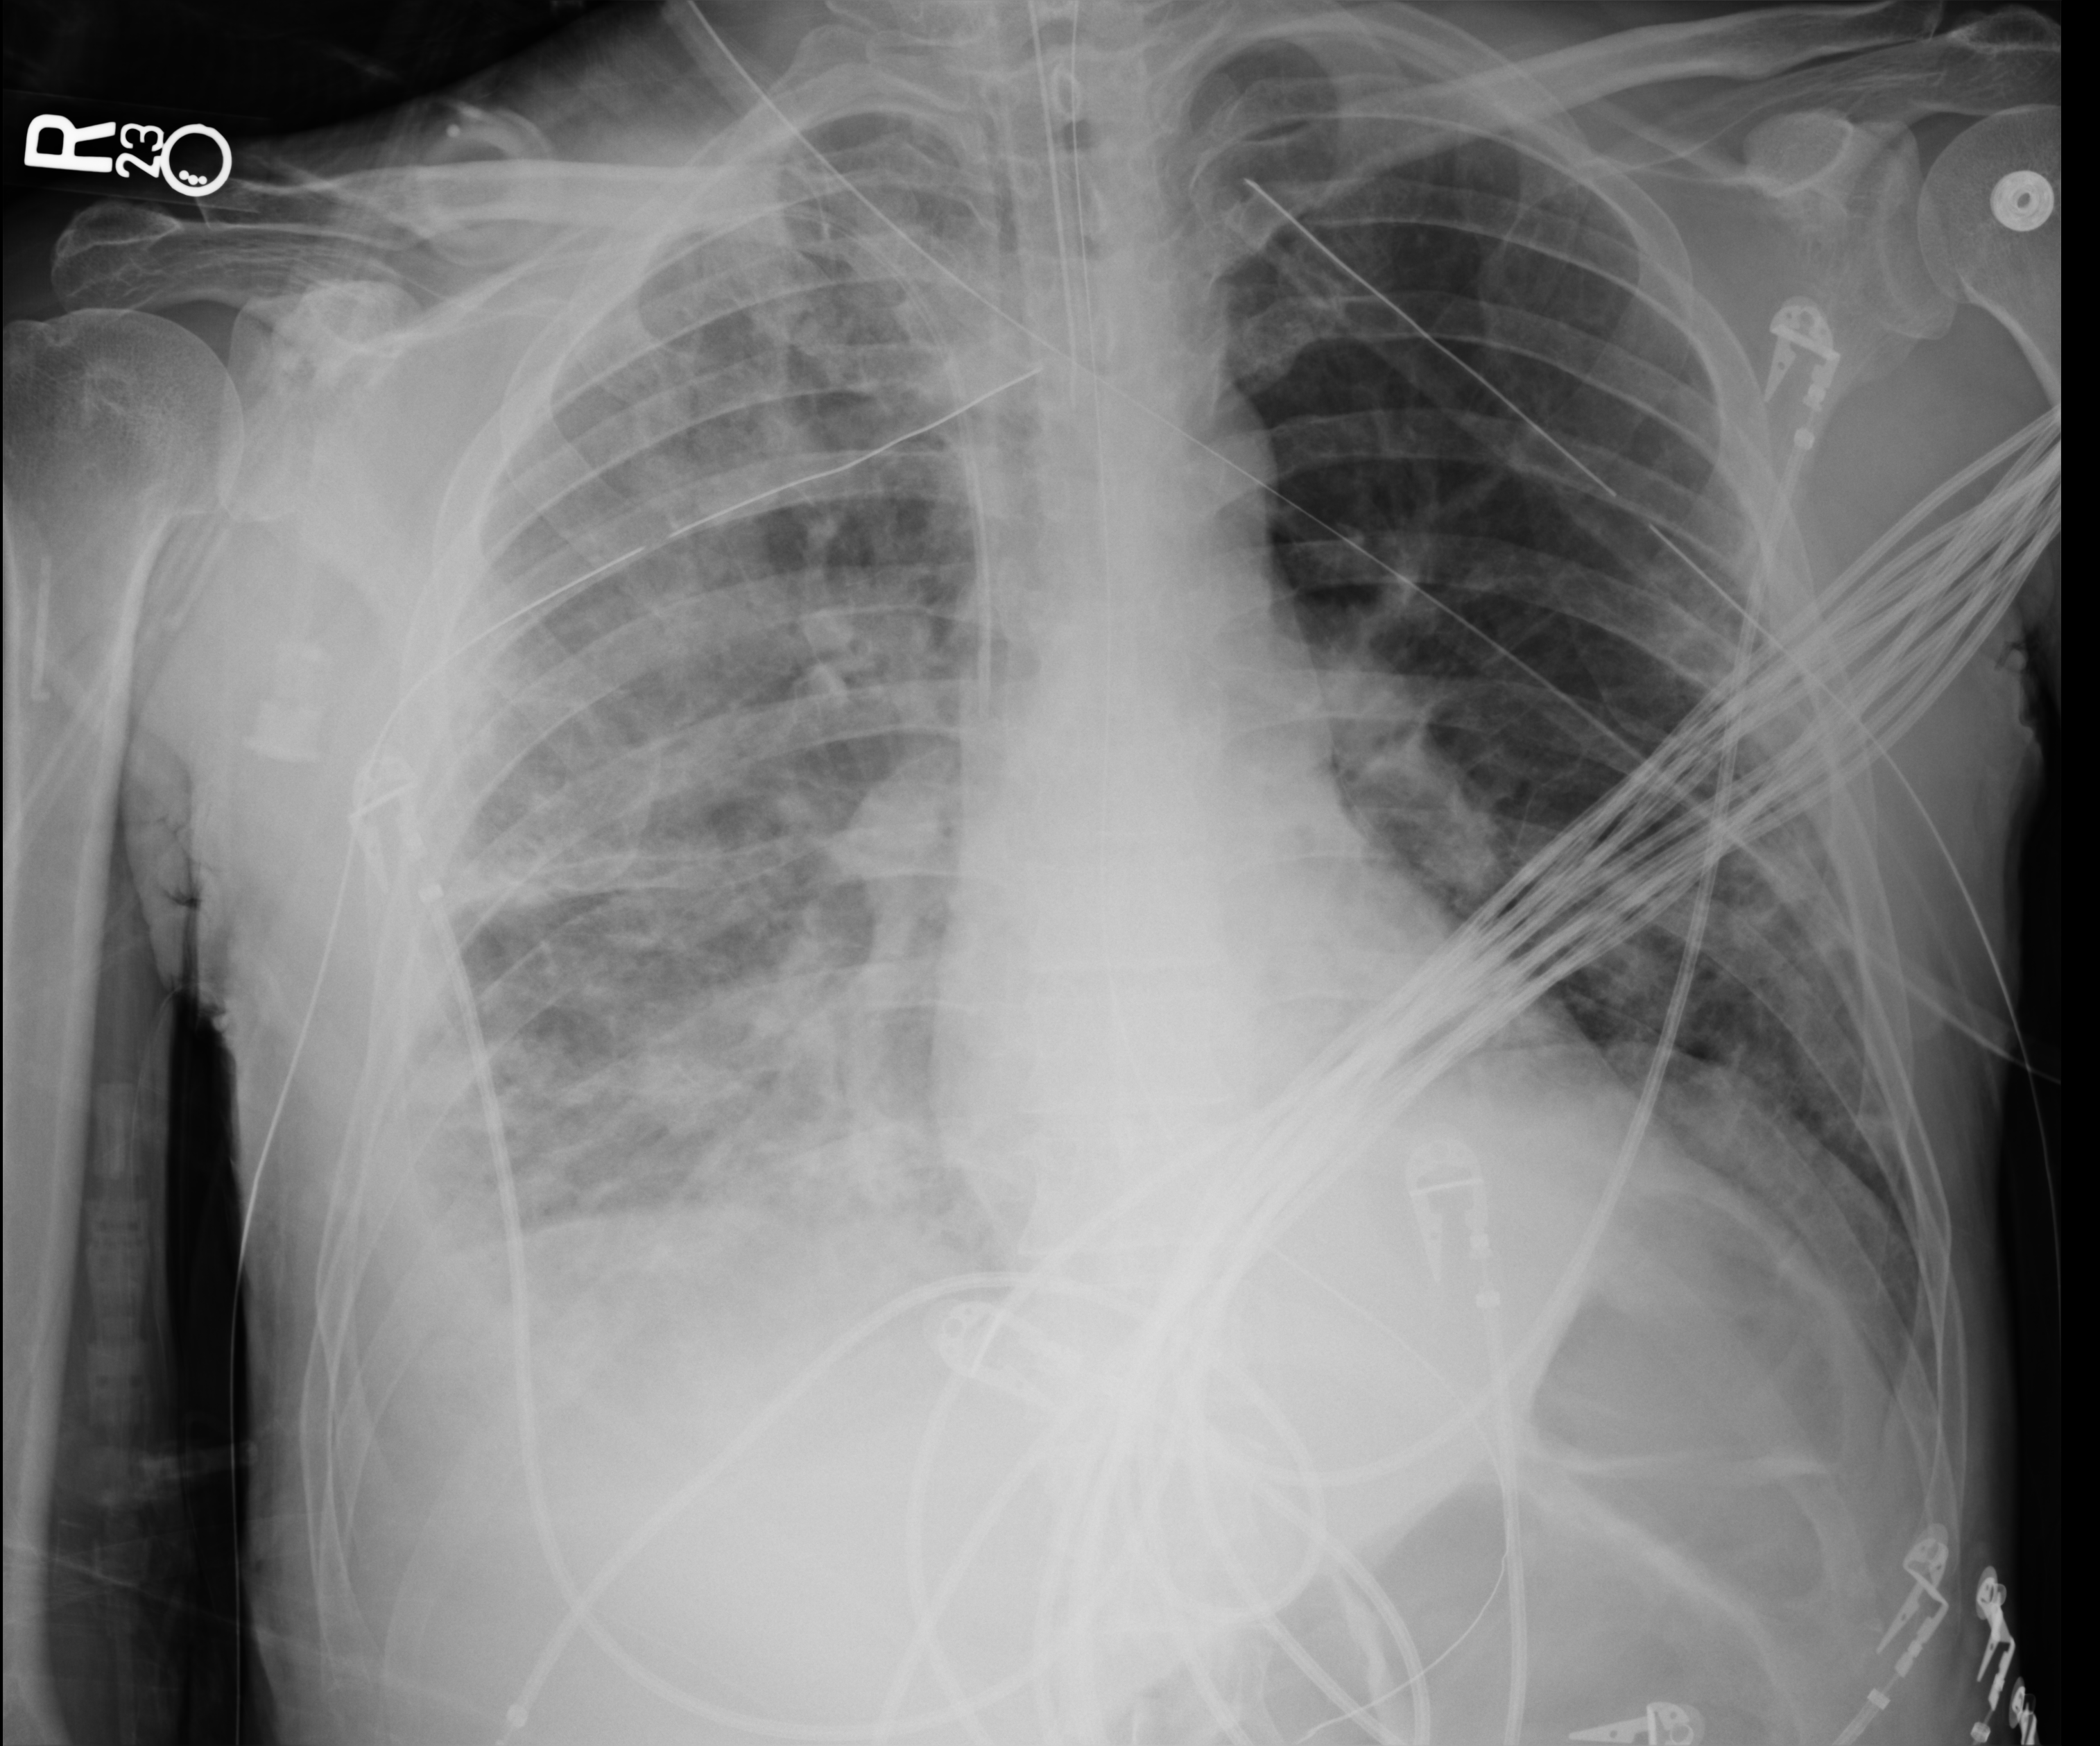
Chest X-ray (portable); anteroposterior (AP) projection. Patient hospitalised with COVID-19; male, aged 18–59 years.
Admission-level facts for this patient (not findings on this image; timing relative to this image not recorded): mechanically ventilated during this hospital stay: yes.